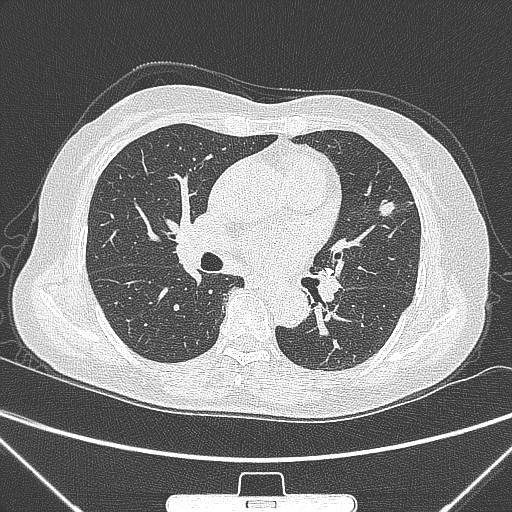
Chest CT, one axial slice. Position 149 of 300 along the scan axis. 120 kVp. Lung window (W 1500 / L -600 HU). 1 mm slice thickness. 512 × 512 image matrix, field of view 350 × 350 mm. Female patient, age 70 years. Case-level facts recorded for this patient, not image findings: clinical TNM (as recorded): T1b N0 M0; histopathological grade: G2.
Outlined on this slice (rectangle marked by the reading radiologist):
- lung tumour (recorded histology: adenocarcinoma): bounding box (x1, y1, x2, y2) in pixels: (375, 195, 396, 220)